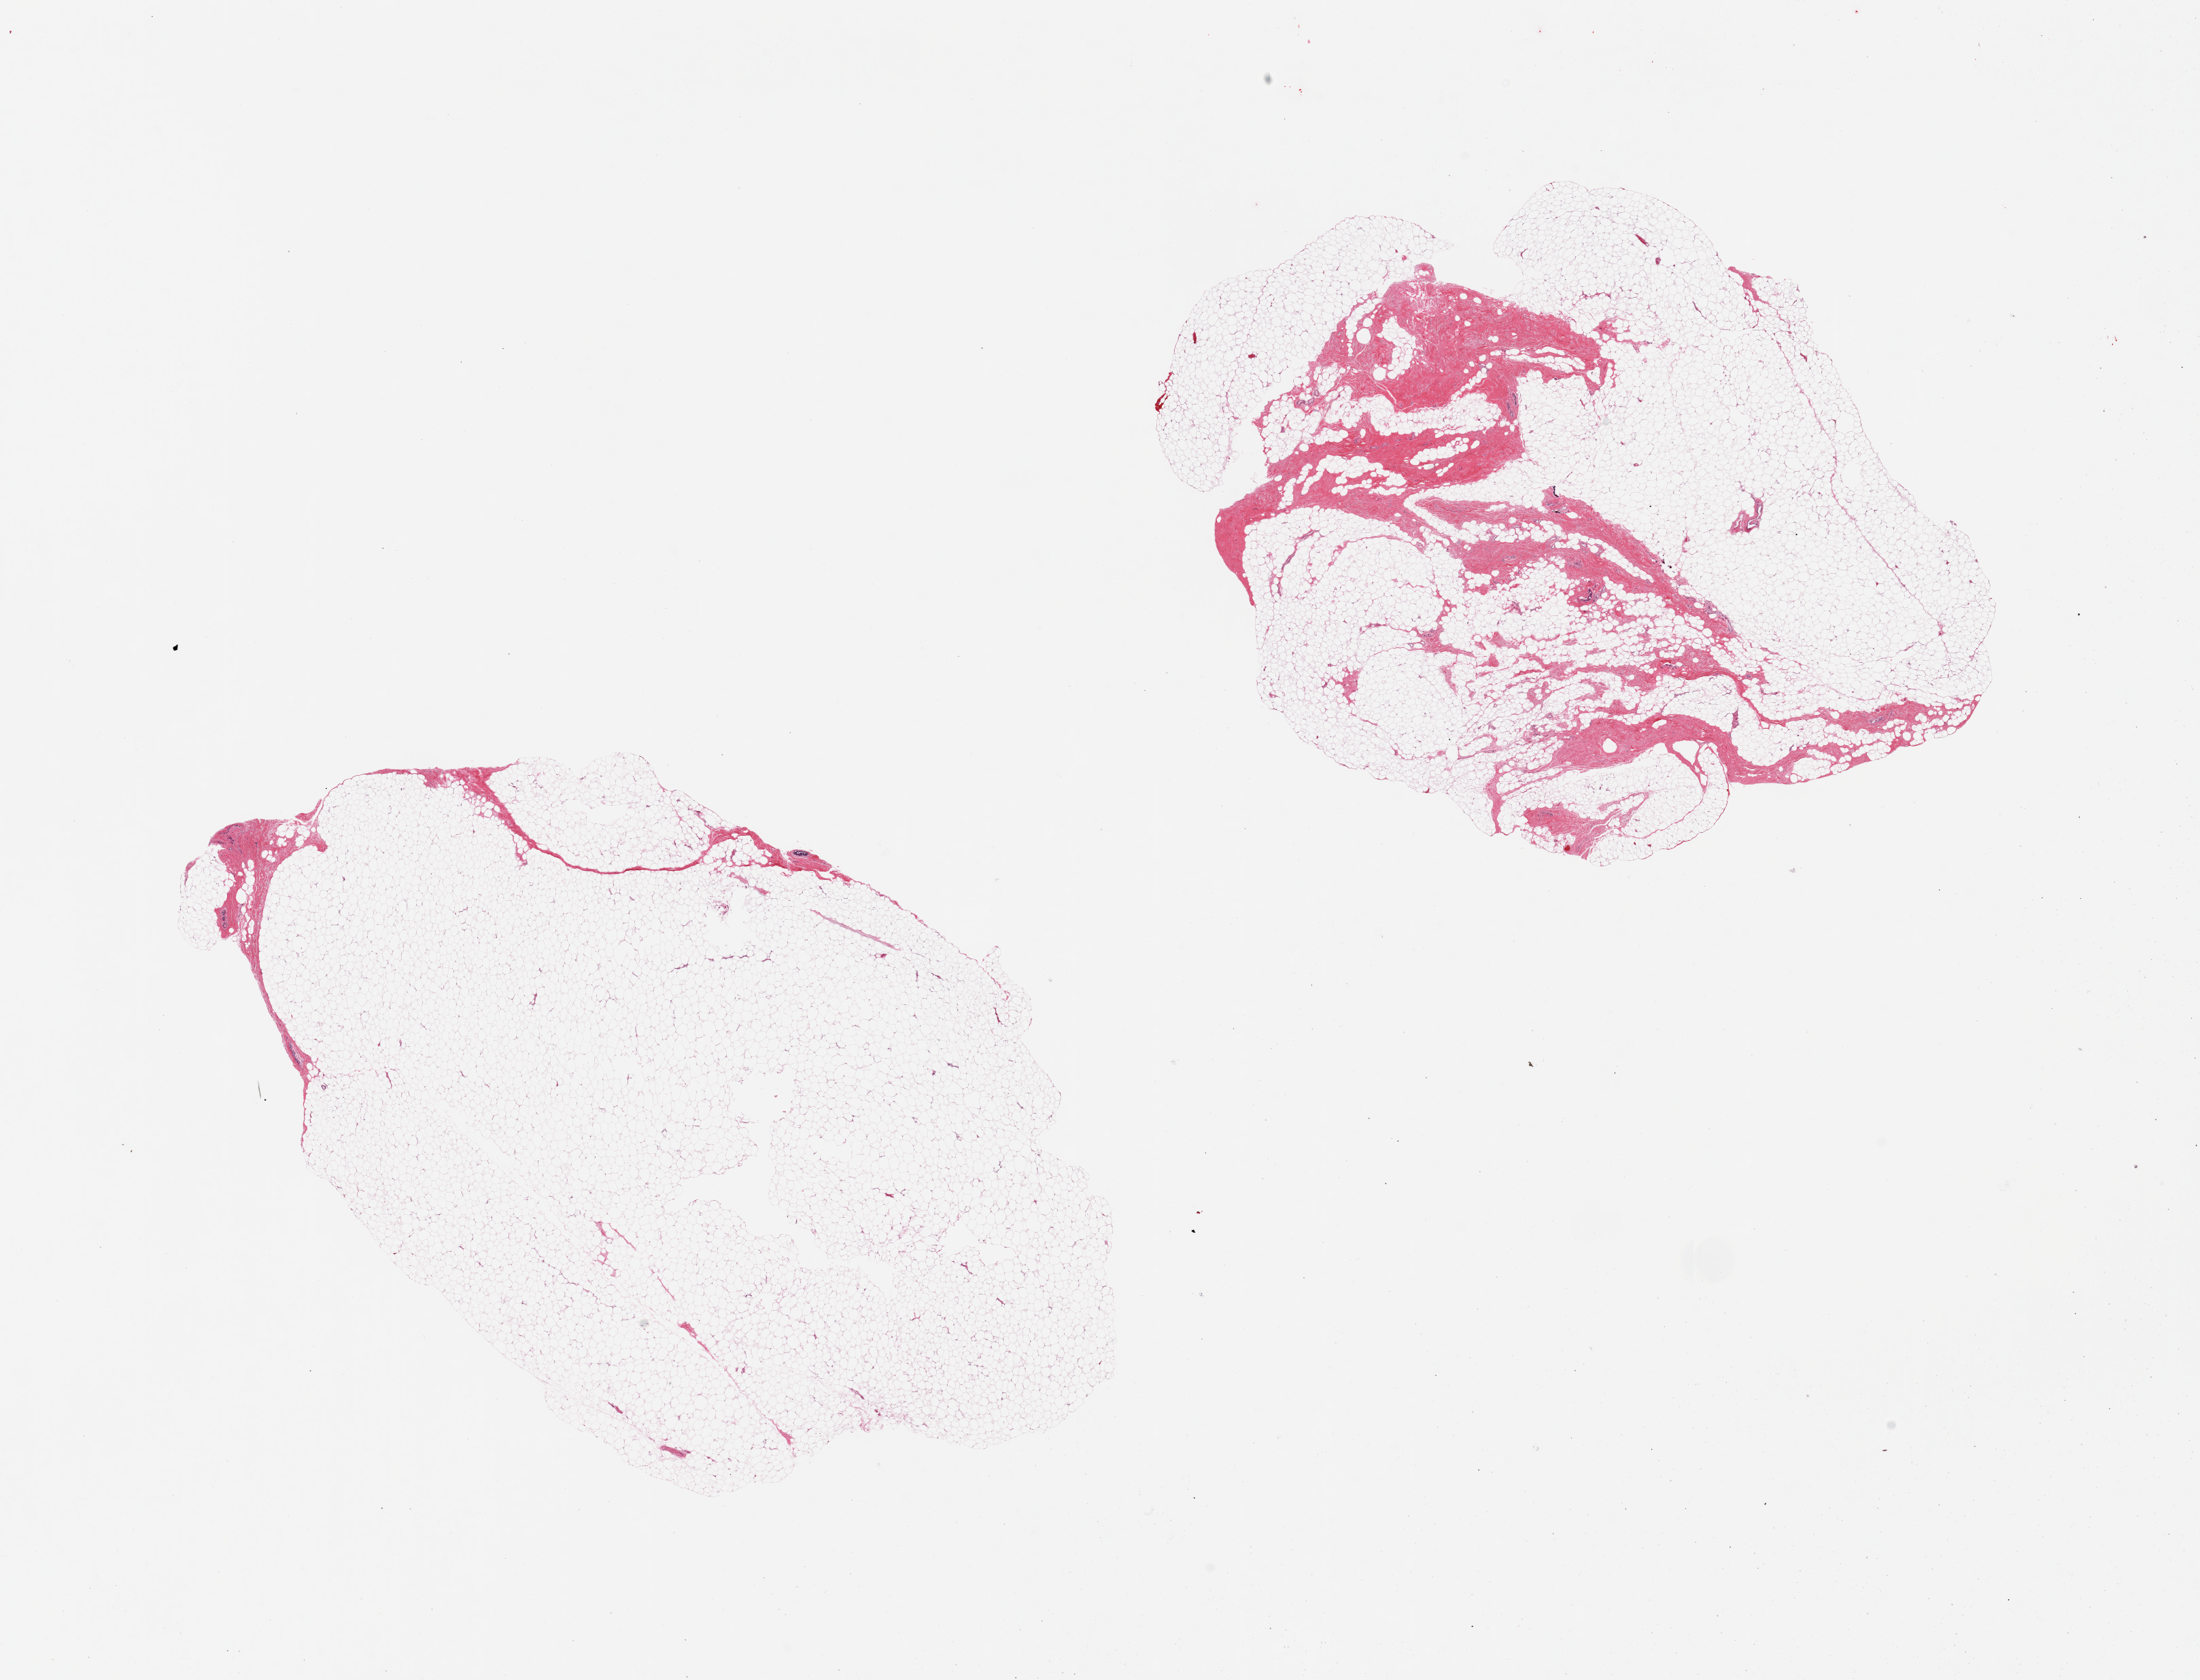
Whole-slide image, hematoxylin and eosin (H&E) stain, brightfield, shown as a low-resolution overview of the whole scanned area (about 25.6 x 19.5 mm, acquisition: 20x scan). PAXgene-fixed paraffin-embedded (PFPE) section. Target tissue: breast. Tissue donor sample. Donor: female.
- reviewer comment on this tissue sample: 2 pieces, predominantly fat with ~10% fibrous stroma combined, limited epithelium present, focal calcification